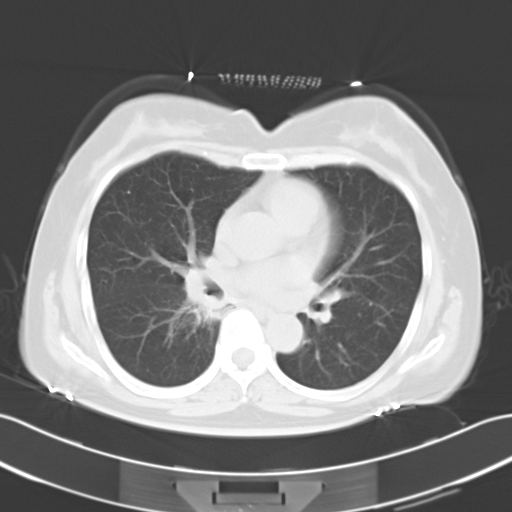
Chest CT, one axial slice. Slice 15 of 27 in the series (ordered by position). Reconstruction kernel B40f. 120 kVp. Lung window (W 1500 / L -600 HU). 512 × 512 image matrix. Female patient, age 59 years. Case-level facts recorded for this patient, not image findings: clinical TNM (as recorded): T1c N0 M1b.
Outlined on this slice (bounding box drawn by a radiologist):
- lung tumour (recorded histology: adenocarcinoma): bounding box <184,291,227,325> (left, top, right, bottom; pixels)